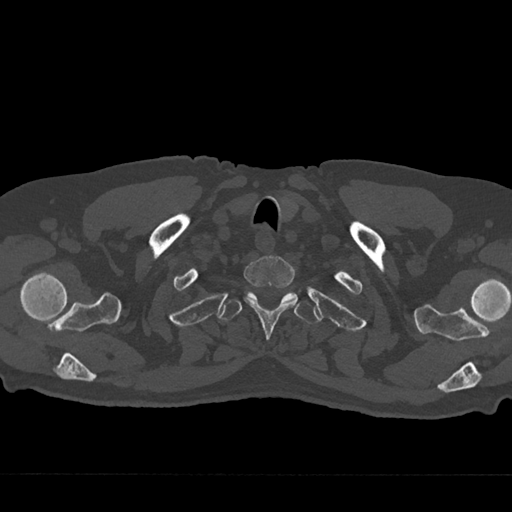
CT including the spine, one axial slice. Slice 640 of 797 in the series (ordered by position). Reconstruction kernel Br40s/3. Bone window (W 1800 / L 400 HU). 0.5 mm slice thickness. 512 × 512 image matrix, field of view 377 × 377 mm. Patient: male, 75 years. Case-level facts recorded for this patient, not image findings: primary cancer: renal; vertebrae with lytic lesions (as recorded): T4.
Outlined on this slice (semi-automatic segmentation, software-assisted and operator-edited):
- T1 vertebra: bounding box (x1, y1, x2, y2) in pixels: (244, 255, 298, 340)
- T2 vertebra: (218, 292, 320, 324)